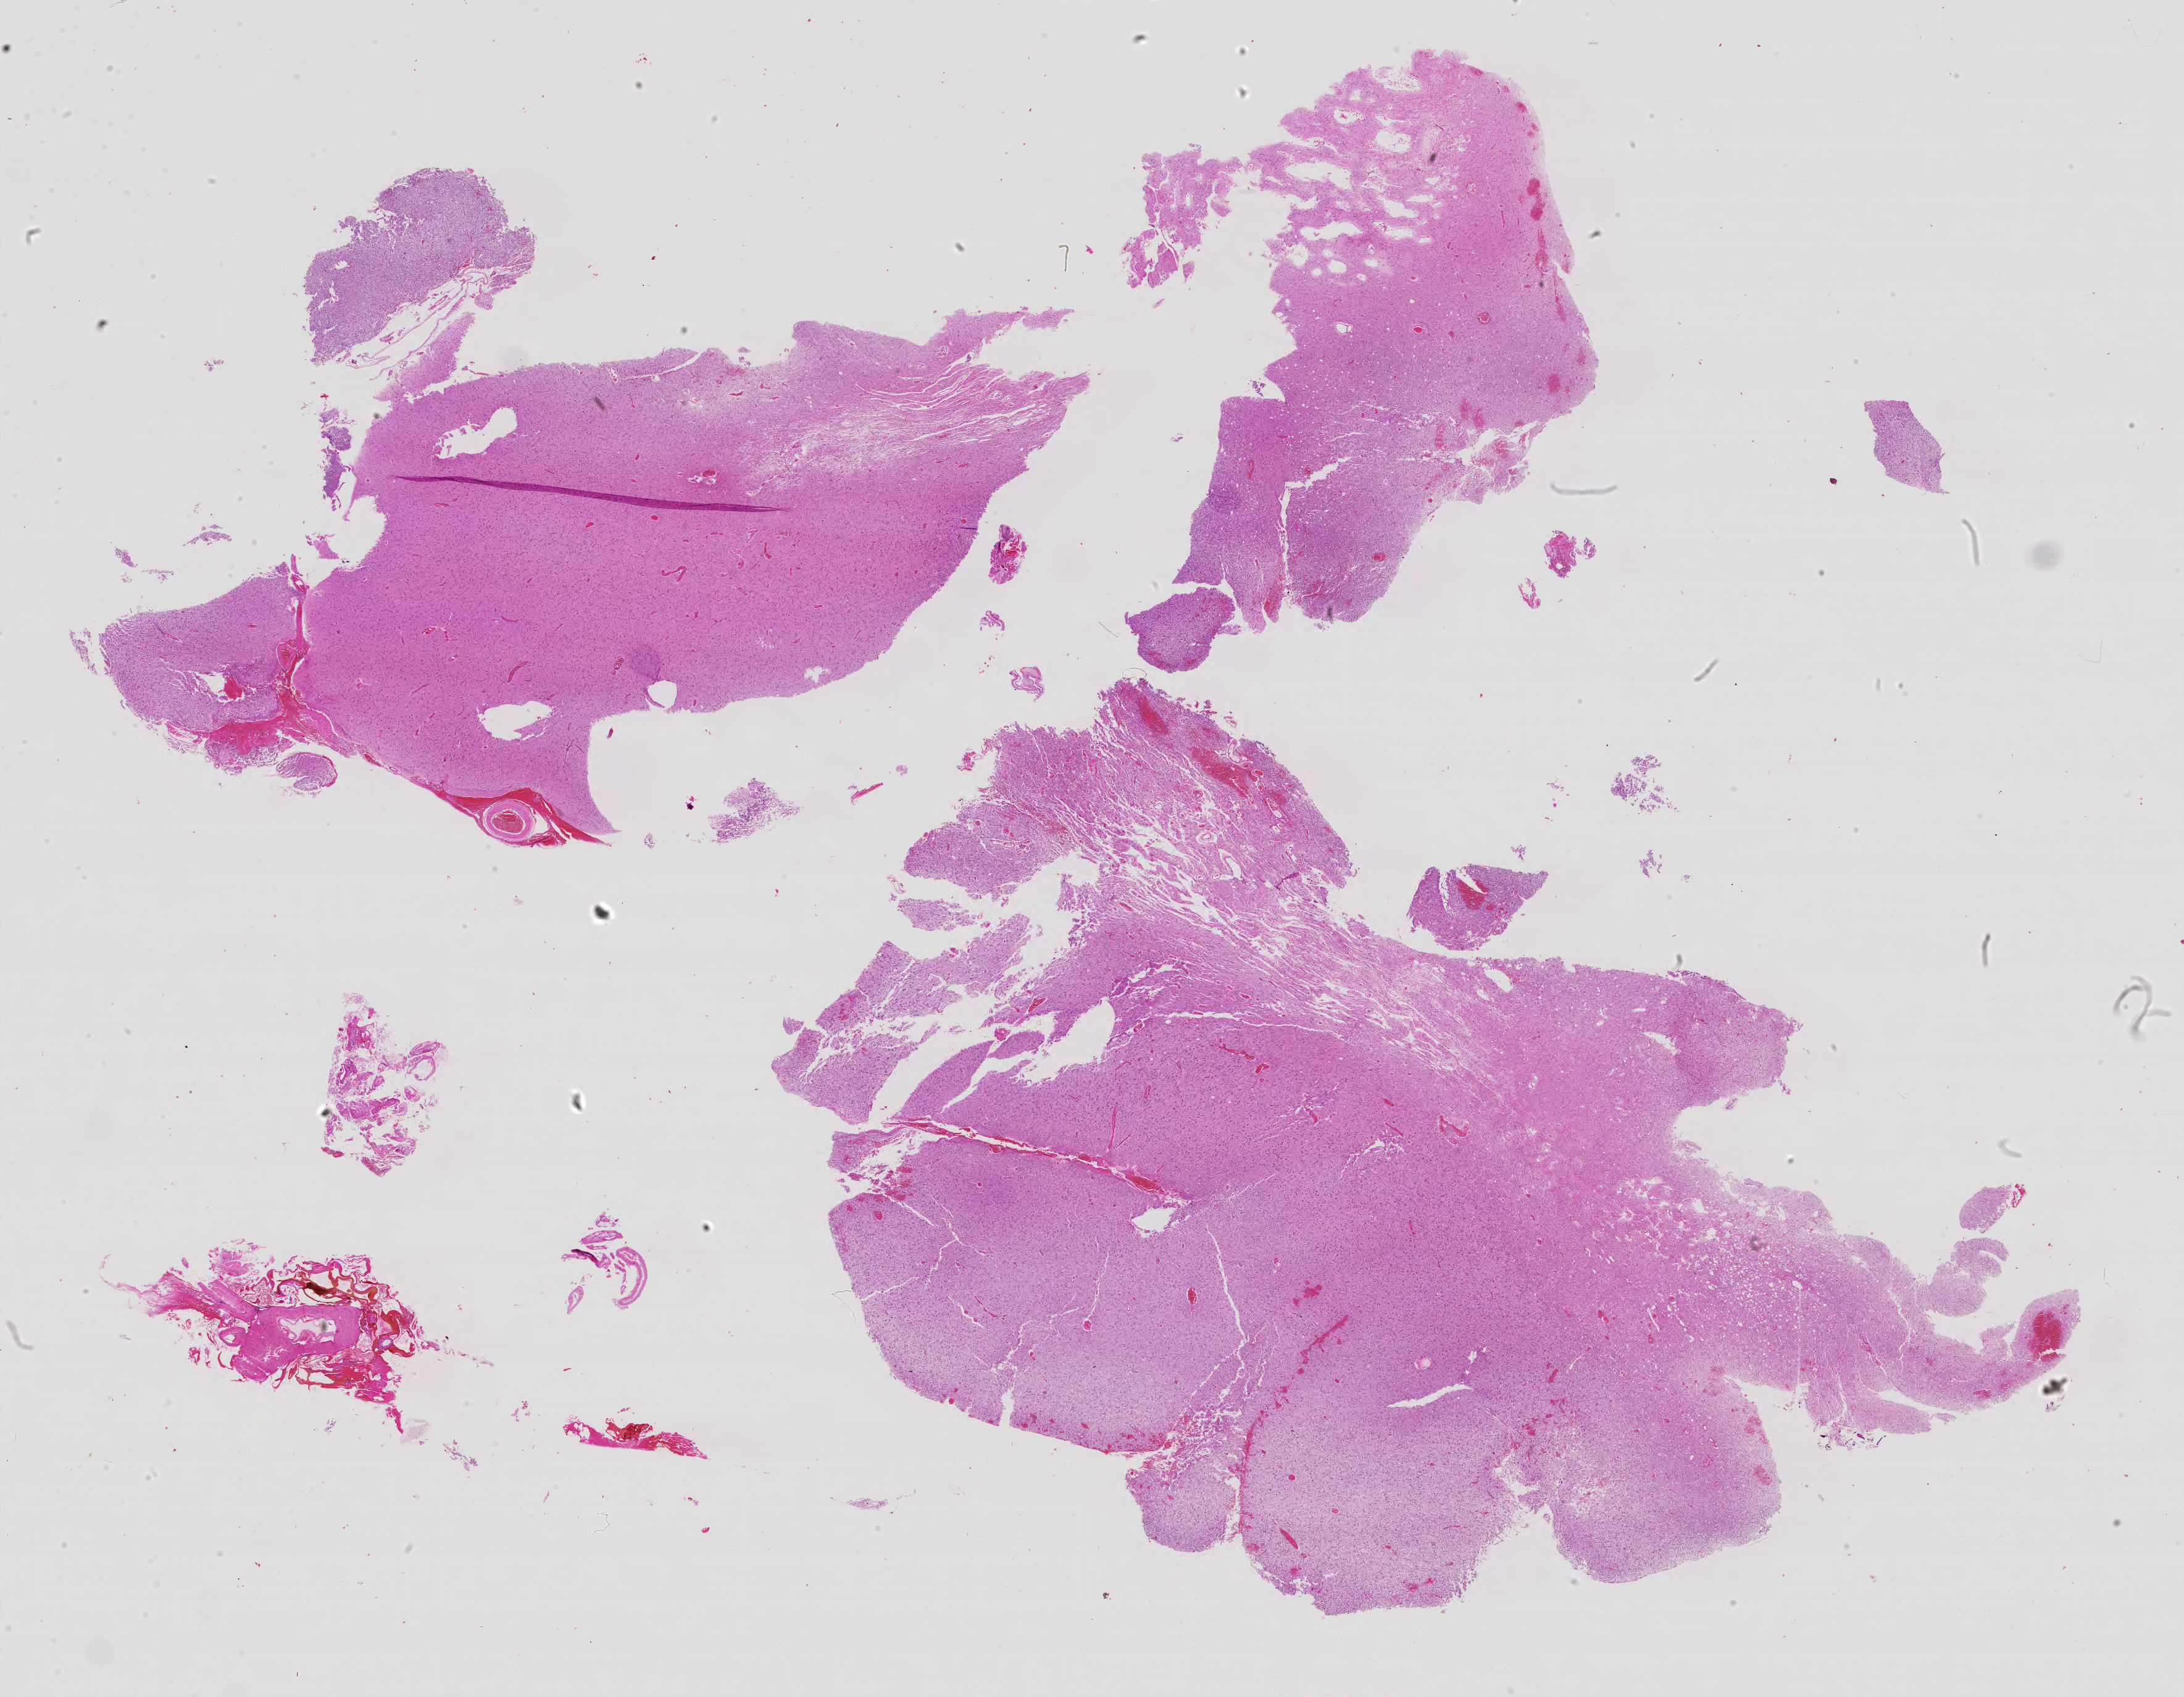
Whole-slide histology image, H&E-stained — a low-resolution overview of the entire scanned area, about 28.3 x 22.0 mm (acquisition: 40x scan). Formalin-fixed paraffin-embedded (FFPE) diagnostic section. Sample: primary tumour, brain. Patient: male, age at initial diagnosis 45 years. Histologic grade: G3 (poorly differentiated).
Pathologic diagnosis: Oligodendroglioma, anaplastic (cerebrum). Laterality: right.